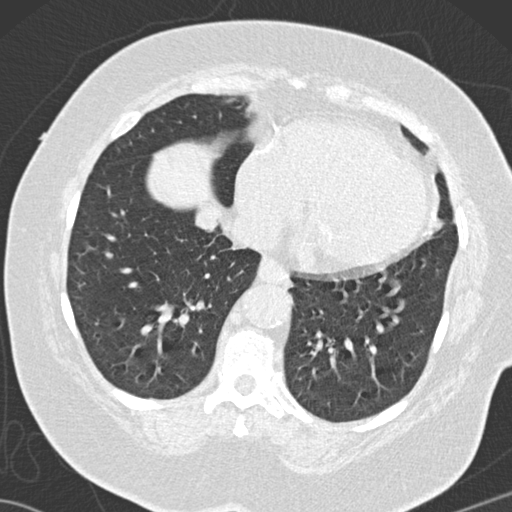
Low-dose screening chest CT, one axial slice; position 46 of 146 along the scan axis; 120 kVp; lung window (W 1500 / L -600 HU); 2 mm slice thickness; 512 × 512 image matrix, field of view 350 × 350 mm.
Structures marked on this image (manually delineated by an expert):
- lesion 3 (tumor, lower lobe of right lung): bounding box (x1, y1, x2, y2) in pixels: (194, 202, 219, 234)